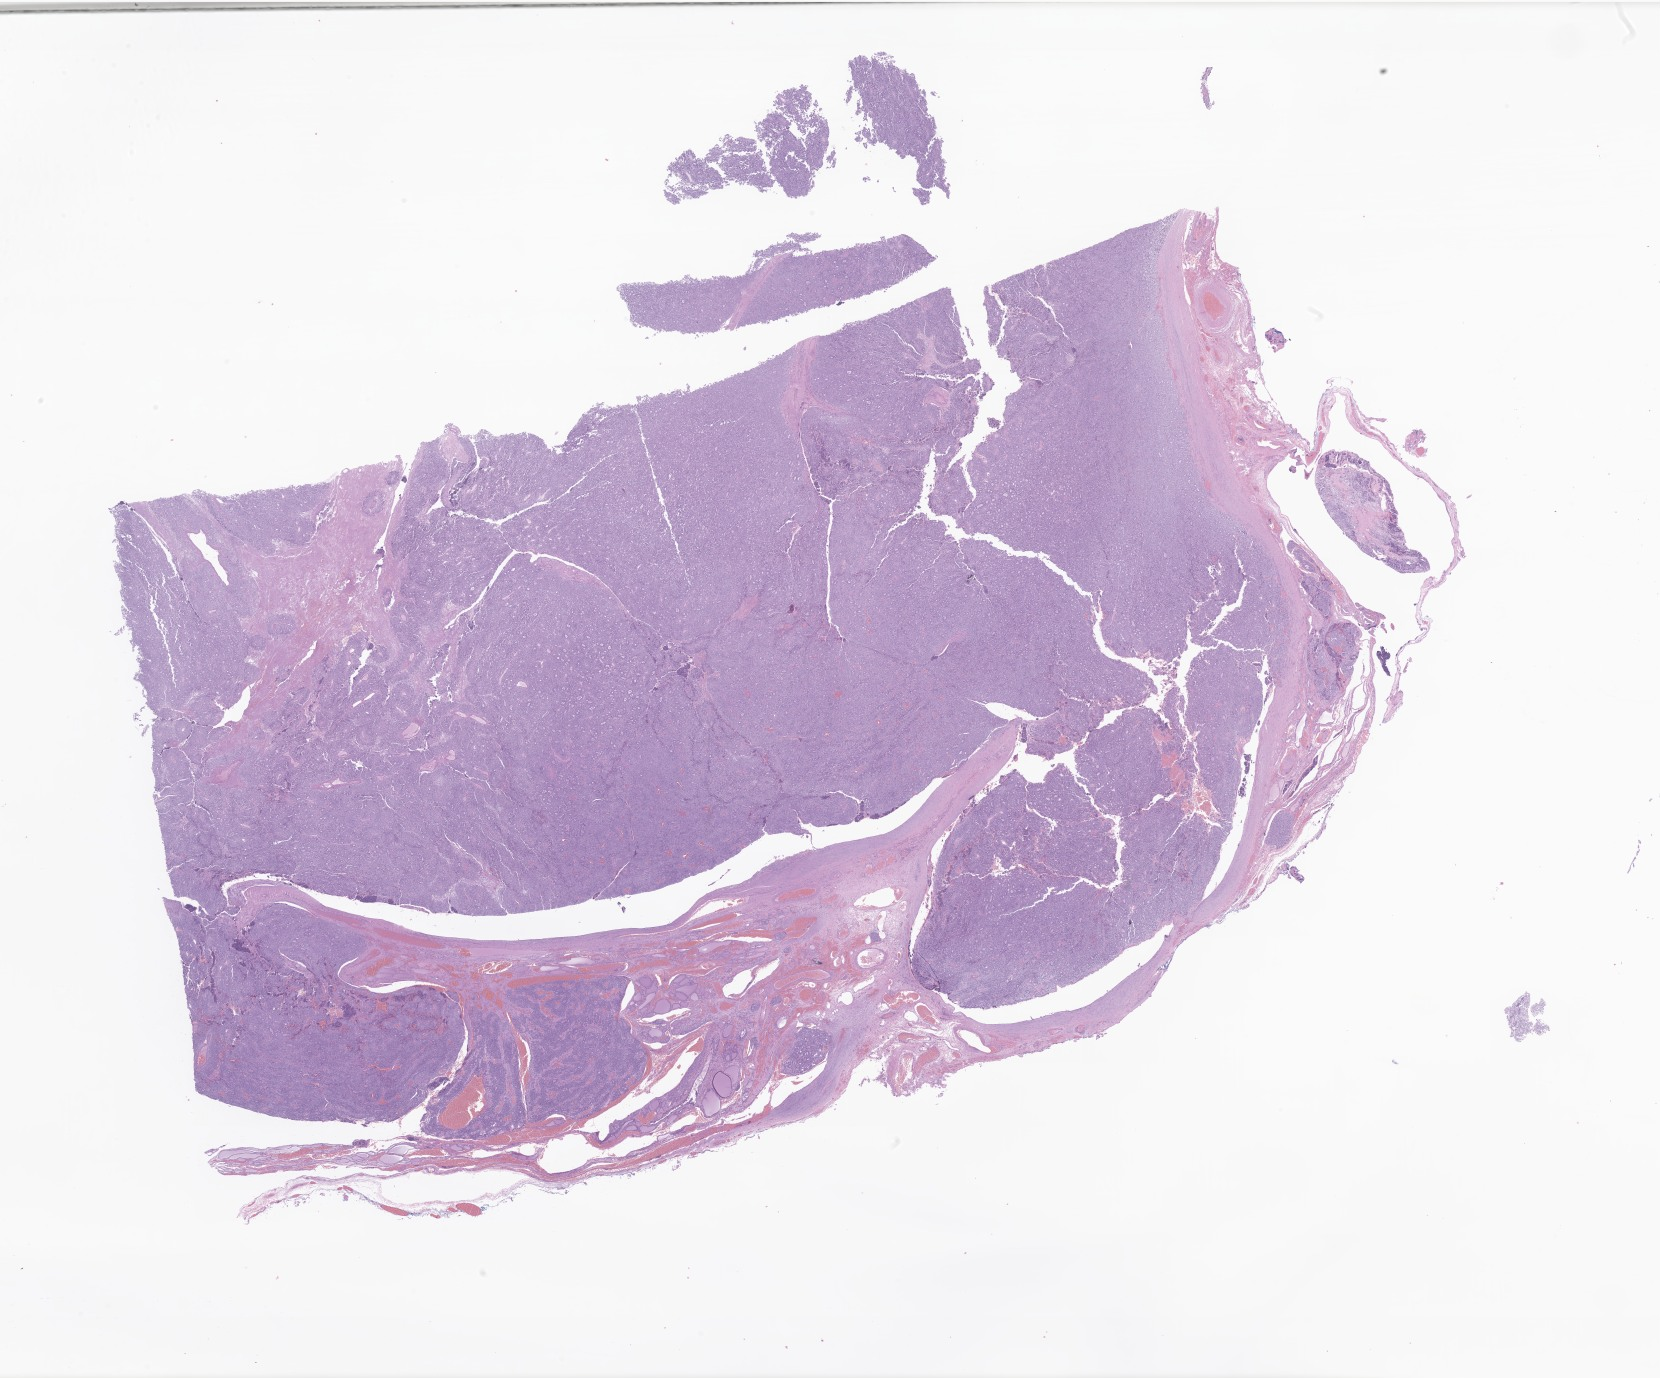
Whole-slide image, hematoxylin and eosin (H&E) stain of tumor tissue from the thyroid, whole scanned area (about 28.0 x 23.2 mm) shown as a low-resolution overview, formalin-fixed, paraffin-embedded (FFPE) tissue. Patient: female, age 190 months.
• diagnosis: Carcinoma, NOS